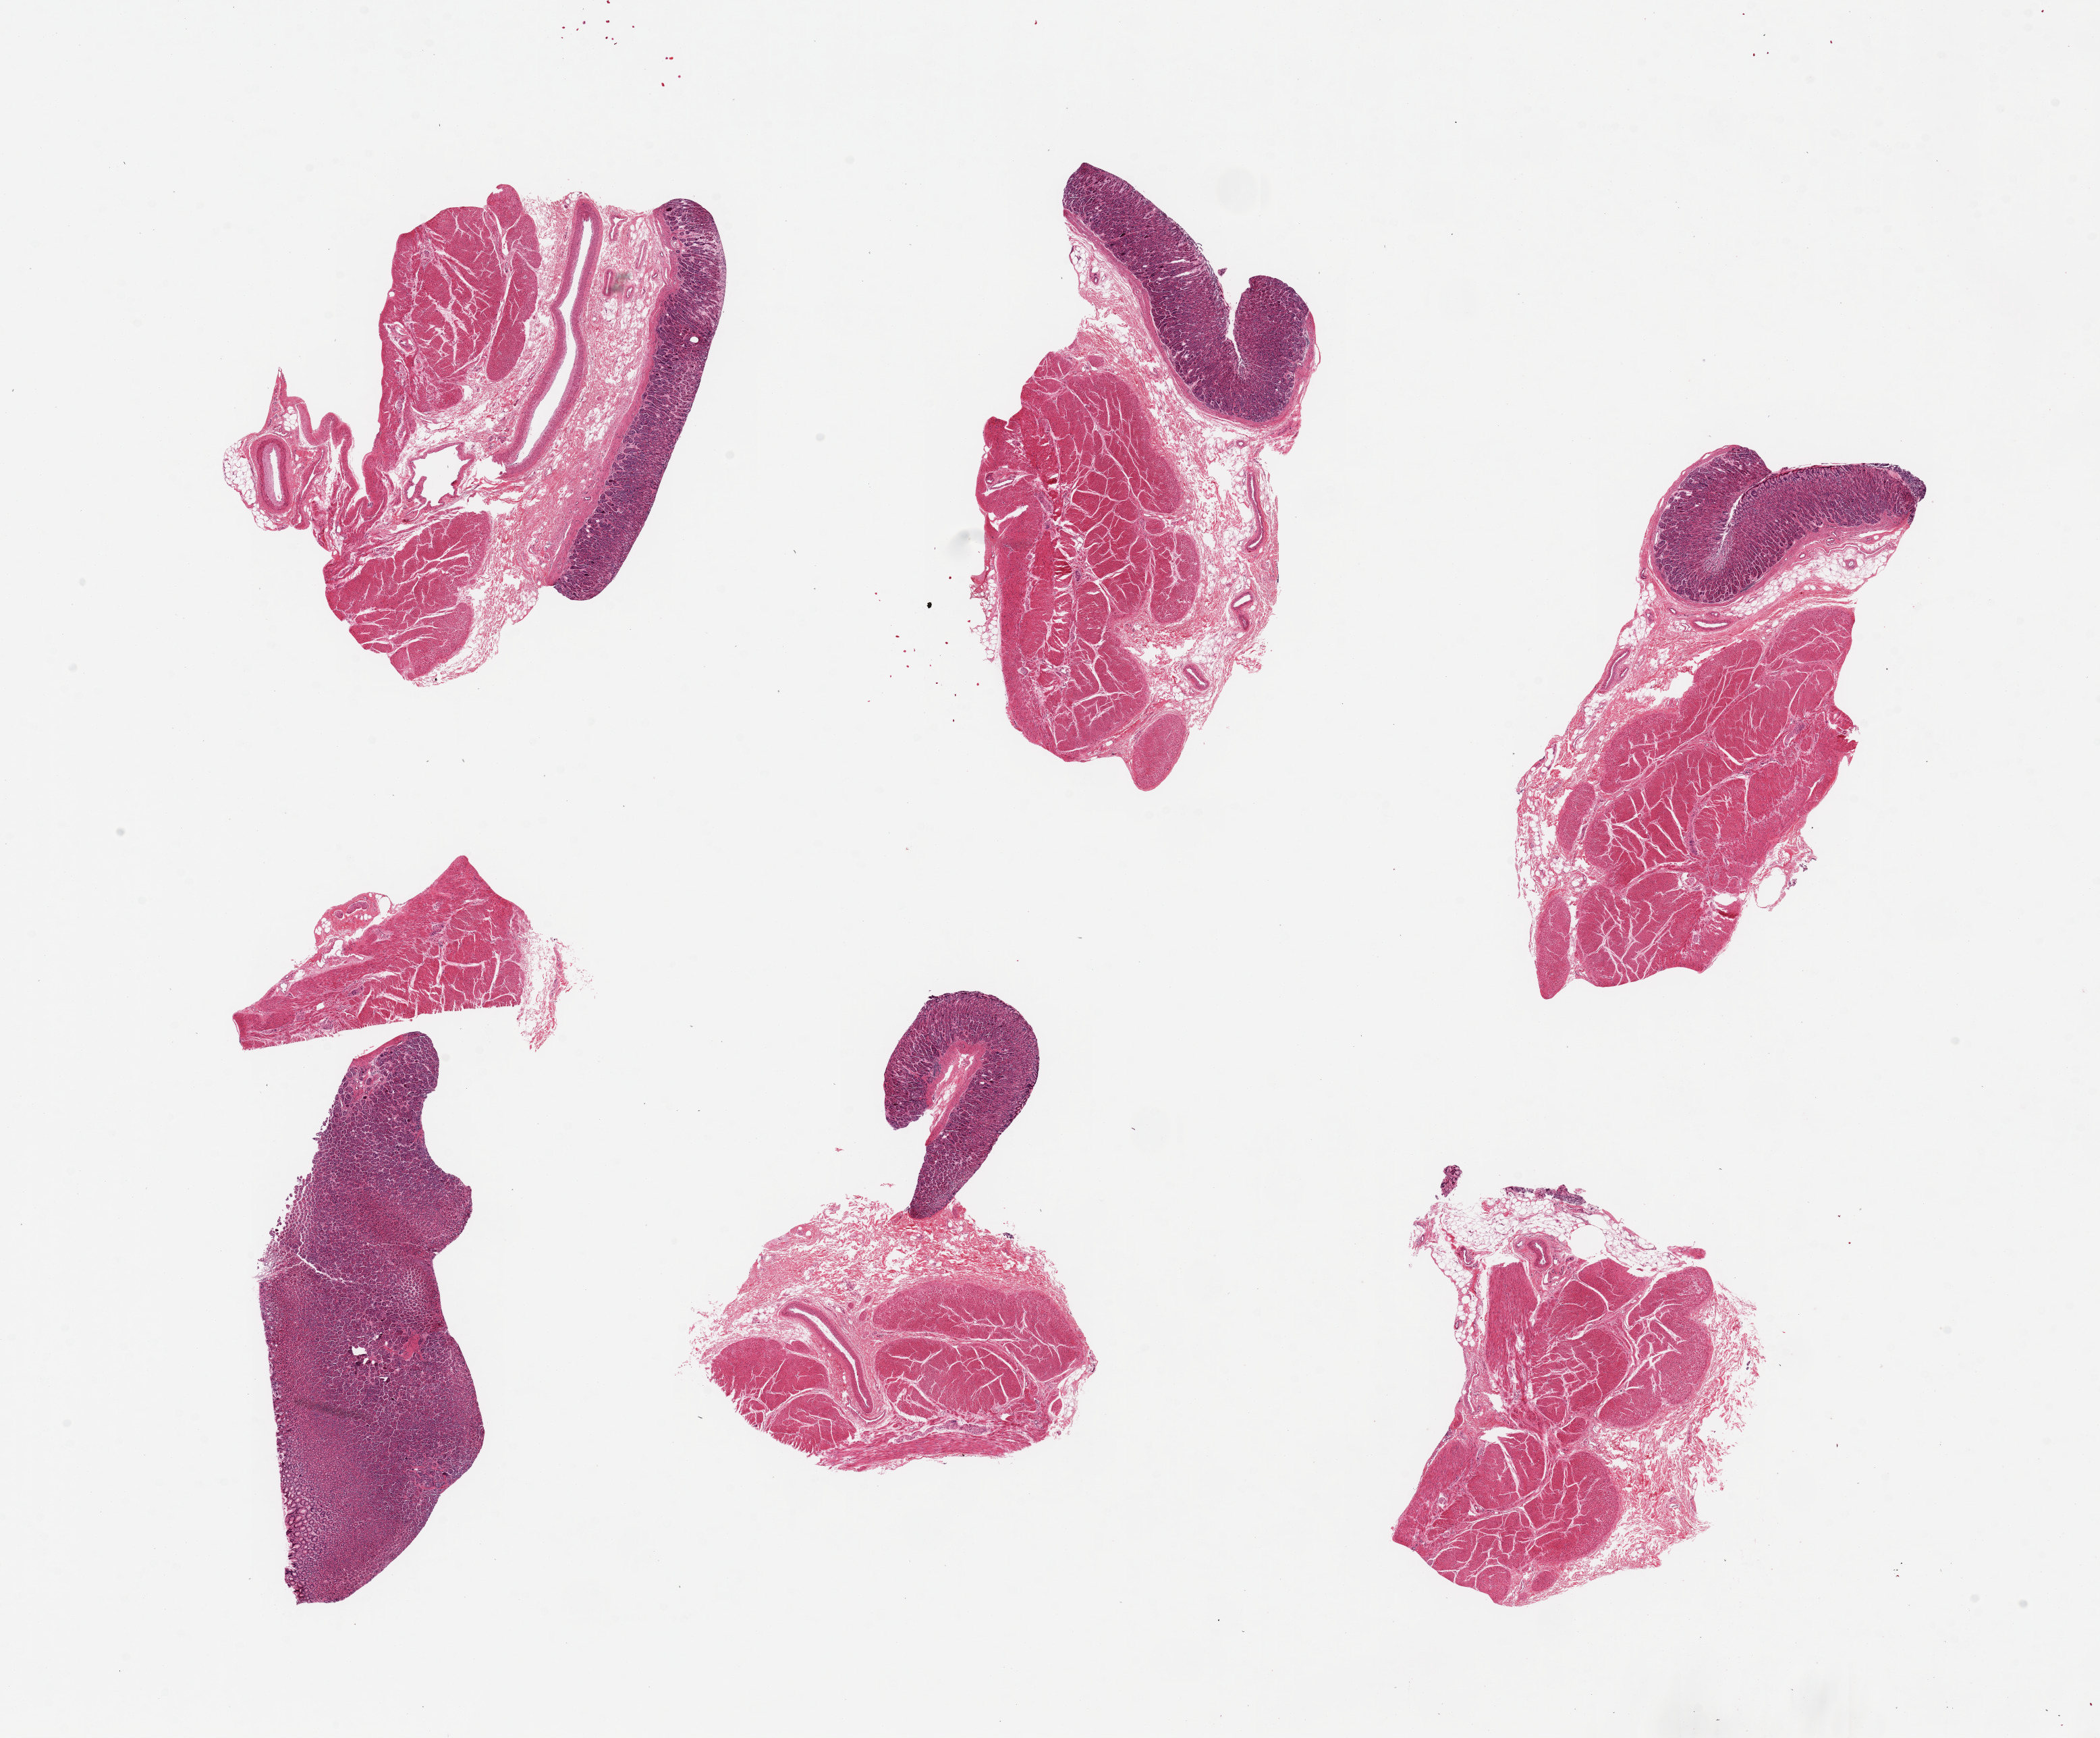
Whole-slide image, H&E stain — a low-resolution overview of the entire scanned area, about 24.6 x 20.4 mm (from a 20x scan); PAXgene-fixed, paraffin-embedded tissue; sampled site (target tissue): stomach; tissue donor sample. Donor: male.
• pathologist's review note for this sample: 6 pieces, ~6x3mm mucosa remarkably well-preserved, up to 600 microns thick